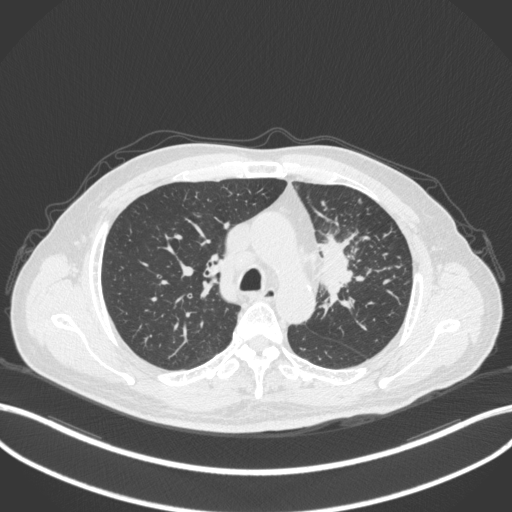
Chest CT, one axial slice. Position 242 of 386 along the scan axis. 120 kVp. Lung window (W 1500 / L -600 HU). 1 mm slice thickness. 512 × 512 image matrix. Male patient, age 69 years. From the clinical record (not read from this slice): clinical TNM (as recorded): T2a N2 M0.
Annotated regions visible in this slice (bounding box drawn by a radiologist):
- lung tumour (recorded histology: adenocarcinoma): bounding box (x1, y1, x2, y2) in pixels: (316, 227, 363, 316)